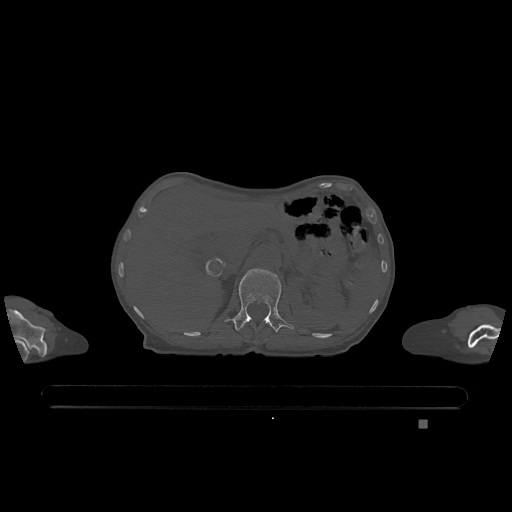
CT including the spine, one axial slice. Position 483 of 1317 along the scan axis. Bone window (W 1800 / L 400 HU). 0.5 mm slice thickness. 512 × 512 image matrix, field of view 500 × 500 mm. Female patient, age 74 years. Case-level facts recorded for this patient, not image findings: primary cancer: lung; vertebrae with lytic lesions (as recorded): T1, T4, T5, T6, L4, L5.
Structures marked on this image (semi-automatically segmented with operator editing):
- L1 vertebra: box from (x=226, y=269) to (x=294, y=333) px